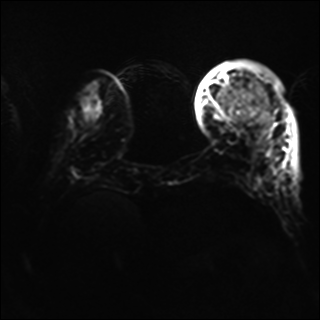
Breast MRI, one axial slice; position 12 of 40 along the scan axis; diffusion-weighted series; image 2 of 4 stored at this slice position (different b-values; order by instance number); 1.5 T; 4 mm slice thickness; 320 × 320 image matrix, field of view 320 × 320 mm. Female patient.
Structures marked on this image (outlined manually by an expert reader):
- tumour on diffusion-weighted imaging: bounding box [x1, y1, x2, y2] px = [237, 93, 259, 116]